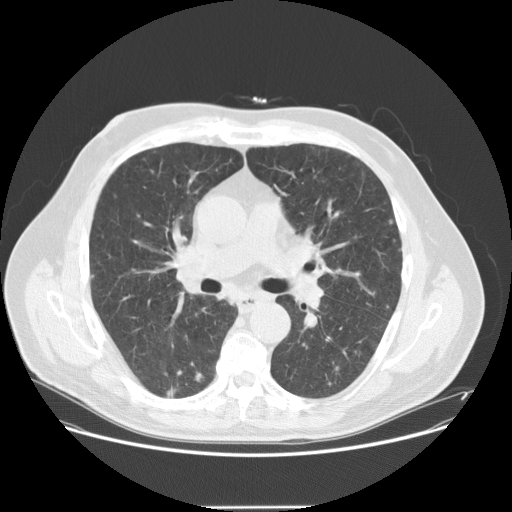
Low-dose screening chest CT, one axial slice. Lung window (W 1500 / L -600 HU). 2.5 mm slice thickness. 512 × 512 image matrix, field of view 400 × 400 mm.
Outlined on this slice (manually delineated by an expert):
- lesion 3 (tumor, lower lobe of right lung): bounding box [x1, y1, x2, y2] px = [166, 386, 176, 397]
- lesion 4 (tumor, lower lobe of right lung): [195, 372, 204, 381]